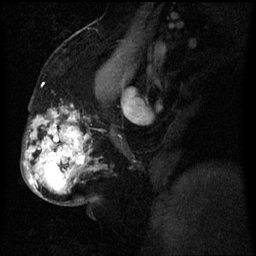
Breast MRI (dynamic contrast-enhanced), one sagittal slice; slice 33 of 60 in the series (ordered by position); dynamic contrast-enhanced series, image 2 of 3 at this slice position (ordered by acquisition); 1.5 T; TE 4.2 ms, TR 8 ms; 2.5 mm slice thickness; 256 × 256 image matrix. Female patient, age 50 years.
Annotated regions visible in this slice (semi-automatic segmentation, software-assisted and operator-edited):
- analysis volume of interest (the breast-tissue region the enhancement analysis was run in; not a lesion): bounding box [x1, y1, x2, y2] px = [27, 112, 86, 201]
- tumour enhancement mask (voxels above the 70 % enhancement threshold inside the analysis volume of interest): [30, 130, 80, 173]